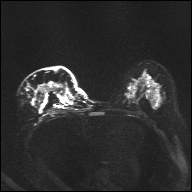
Breast MRI, one axial slice. Slice 20 of 32 in the series (ordered by position). Diffusion-weighted series; image 2 of 4 stored at this slice position (different b-values; order by instance number). 1.5 T. 4 mm slice thickness. 192 × 192 image matrix, field of view 360 × 360 mm. Female patient.
Outlined on this slice (manually delineated by an expert):
- tumour on diffusion-weighted imaging: bounding box [x1, y1, x2, y2] px = [35, 83, 63, 107]